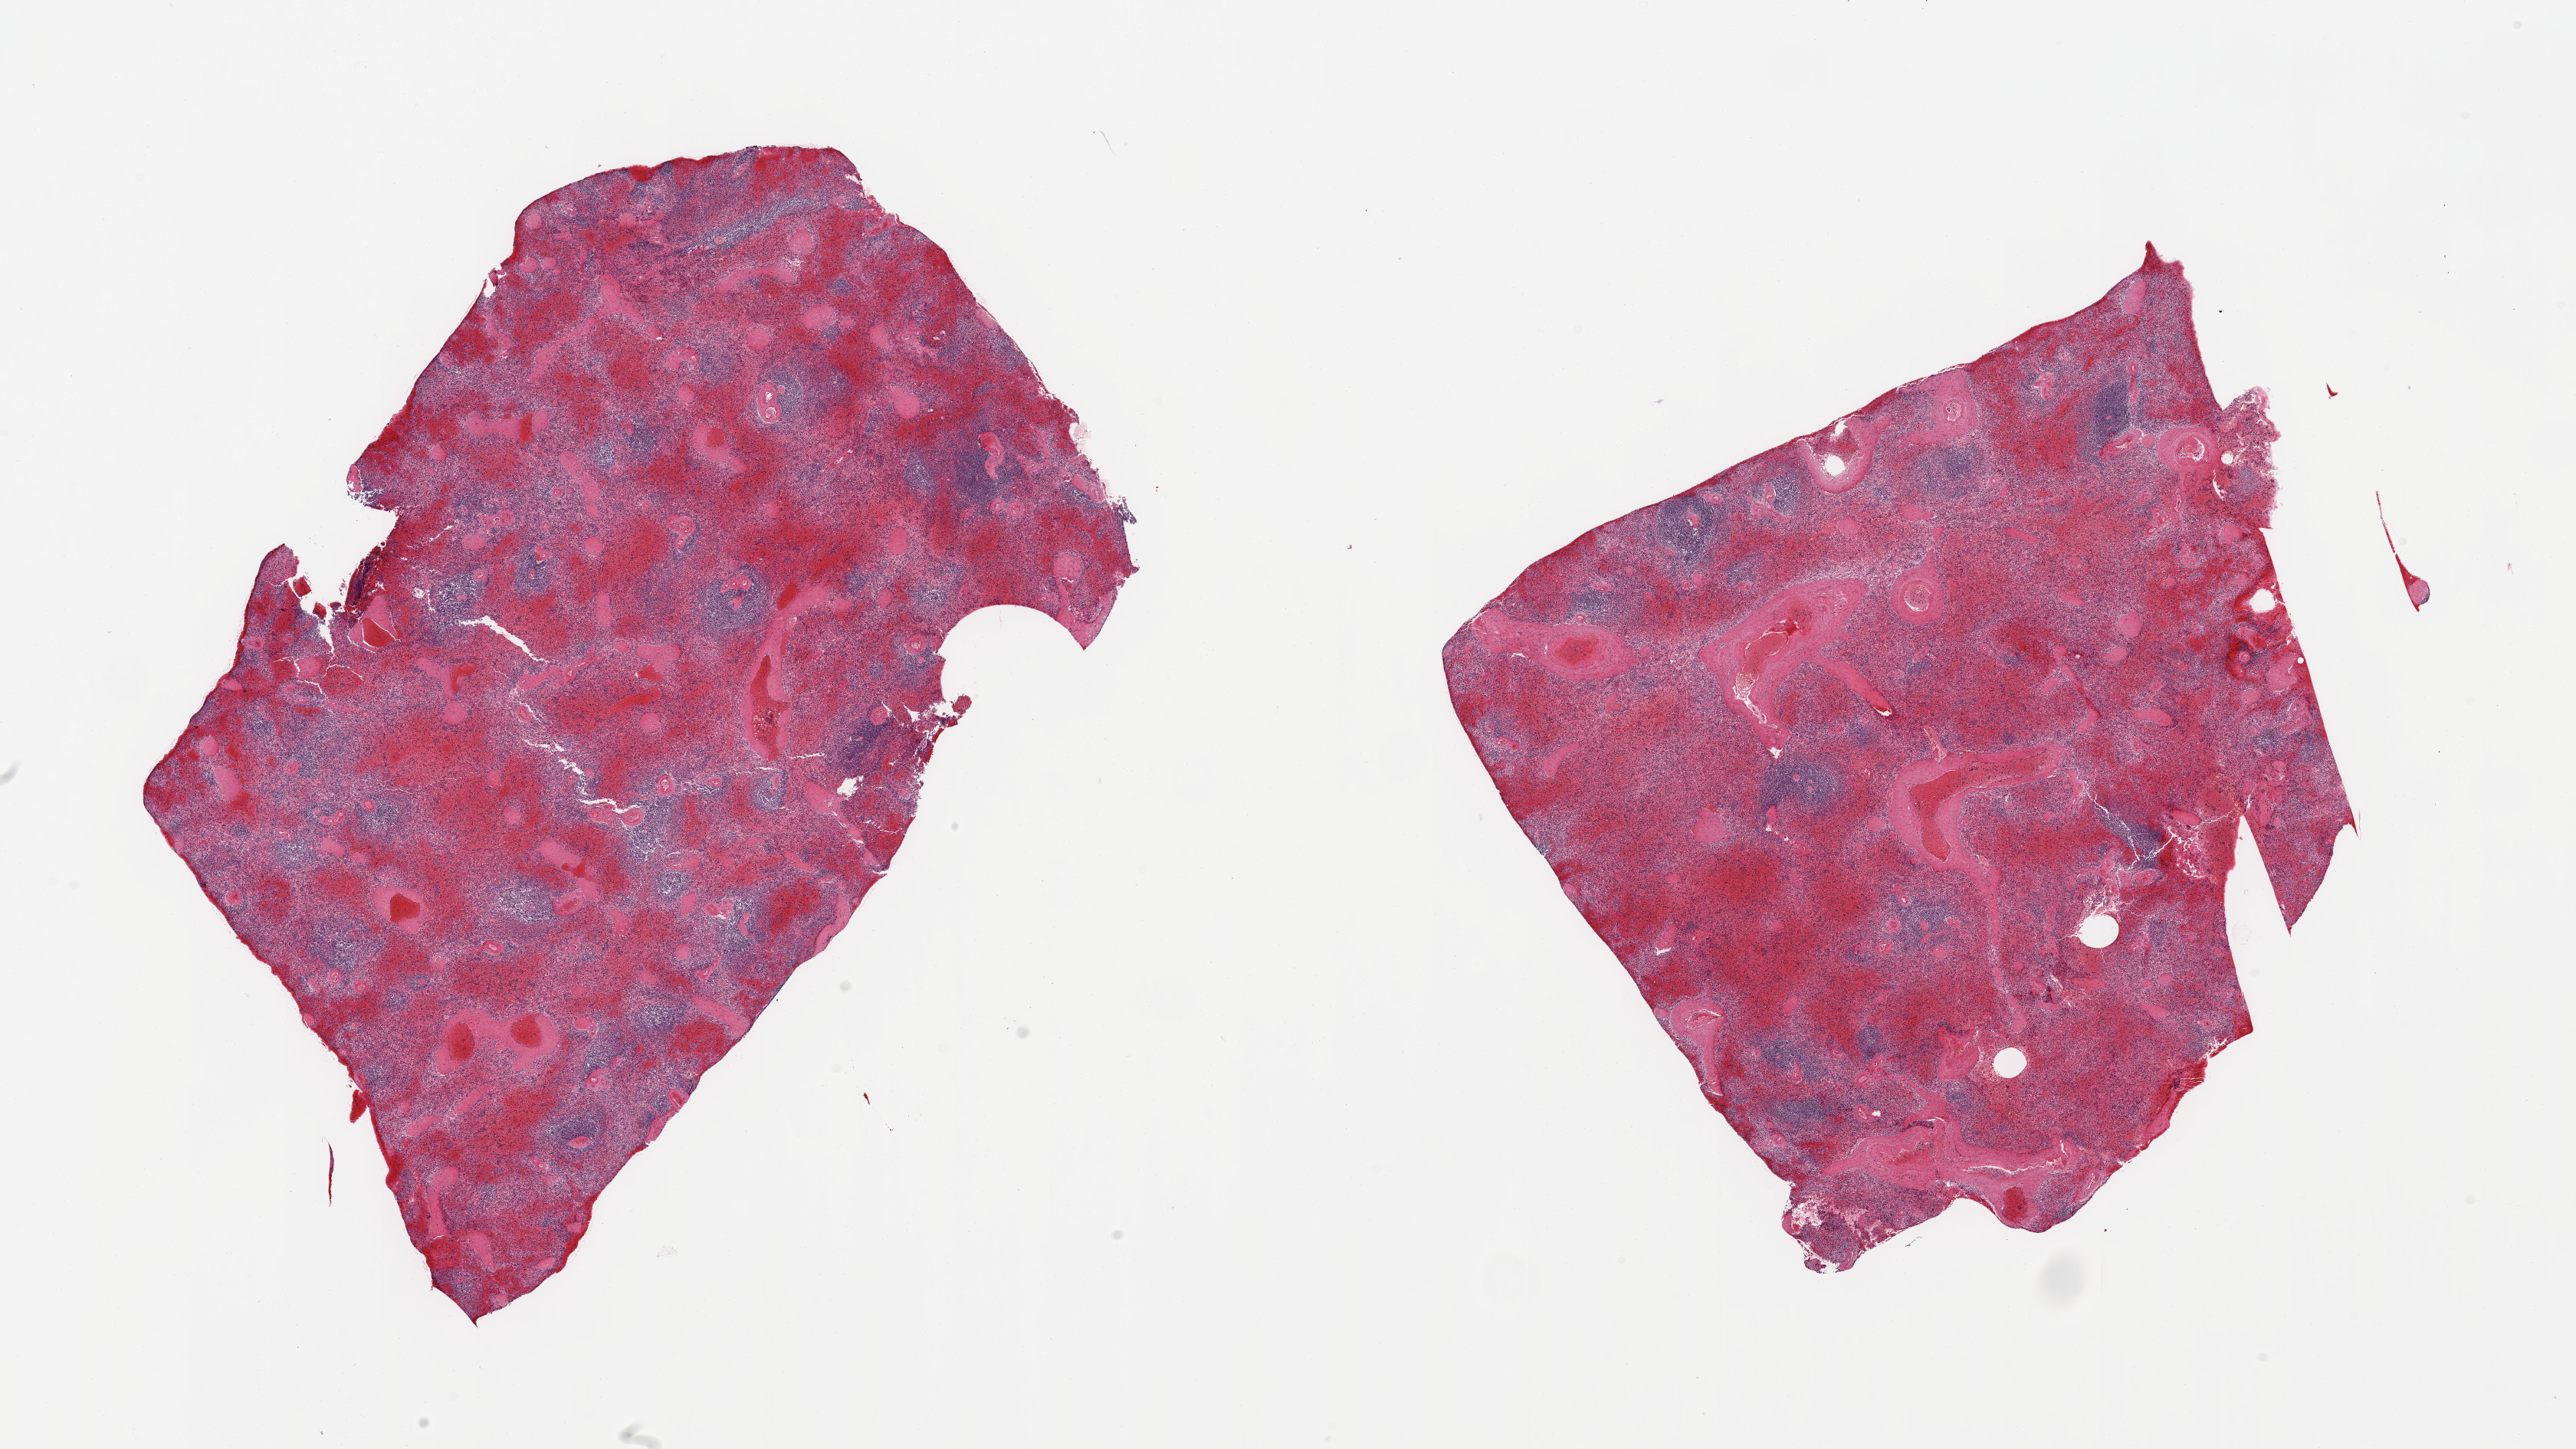
Whole-slide image, H&E stain, brightfield, a low-resolution overview of the entire scanned area, about 26.6 x 15.0 mm (from a 20x scan), PAXgene-fixed, paraffin-embedded tissue, section of spleen (target tissue), donor tissue sample. Donor: male.
Pathologist's review note for this sample: 2 pieces; congested.